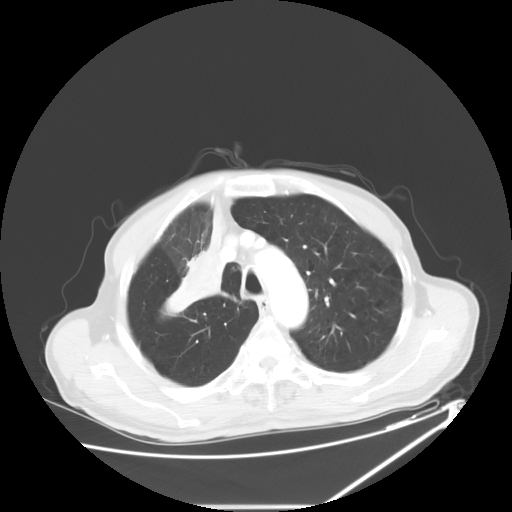
Chest CT, one axial slice; position 47 of 60 along the scan axis; 120 kVp; lung window (W 1500 / L -600 HU); 5 mm slice thickness; 512 × 512 image matrix, field of view 410 × 410 mm. Patient: male, 73 years. Case-level facts recorded for this patient, not image findings: clinical TNM (as recorded): T2a N1 M0.
Structures marked on this image (bounding box drawn by a radiologist):
- lung tumour (recorded histology: squamous cell carcinoma): bounding box (x1, y1, x2, y2) in pixels: (167, 190, 229, 327)